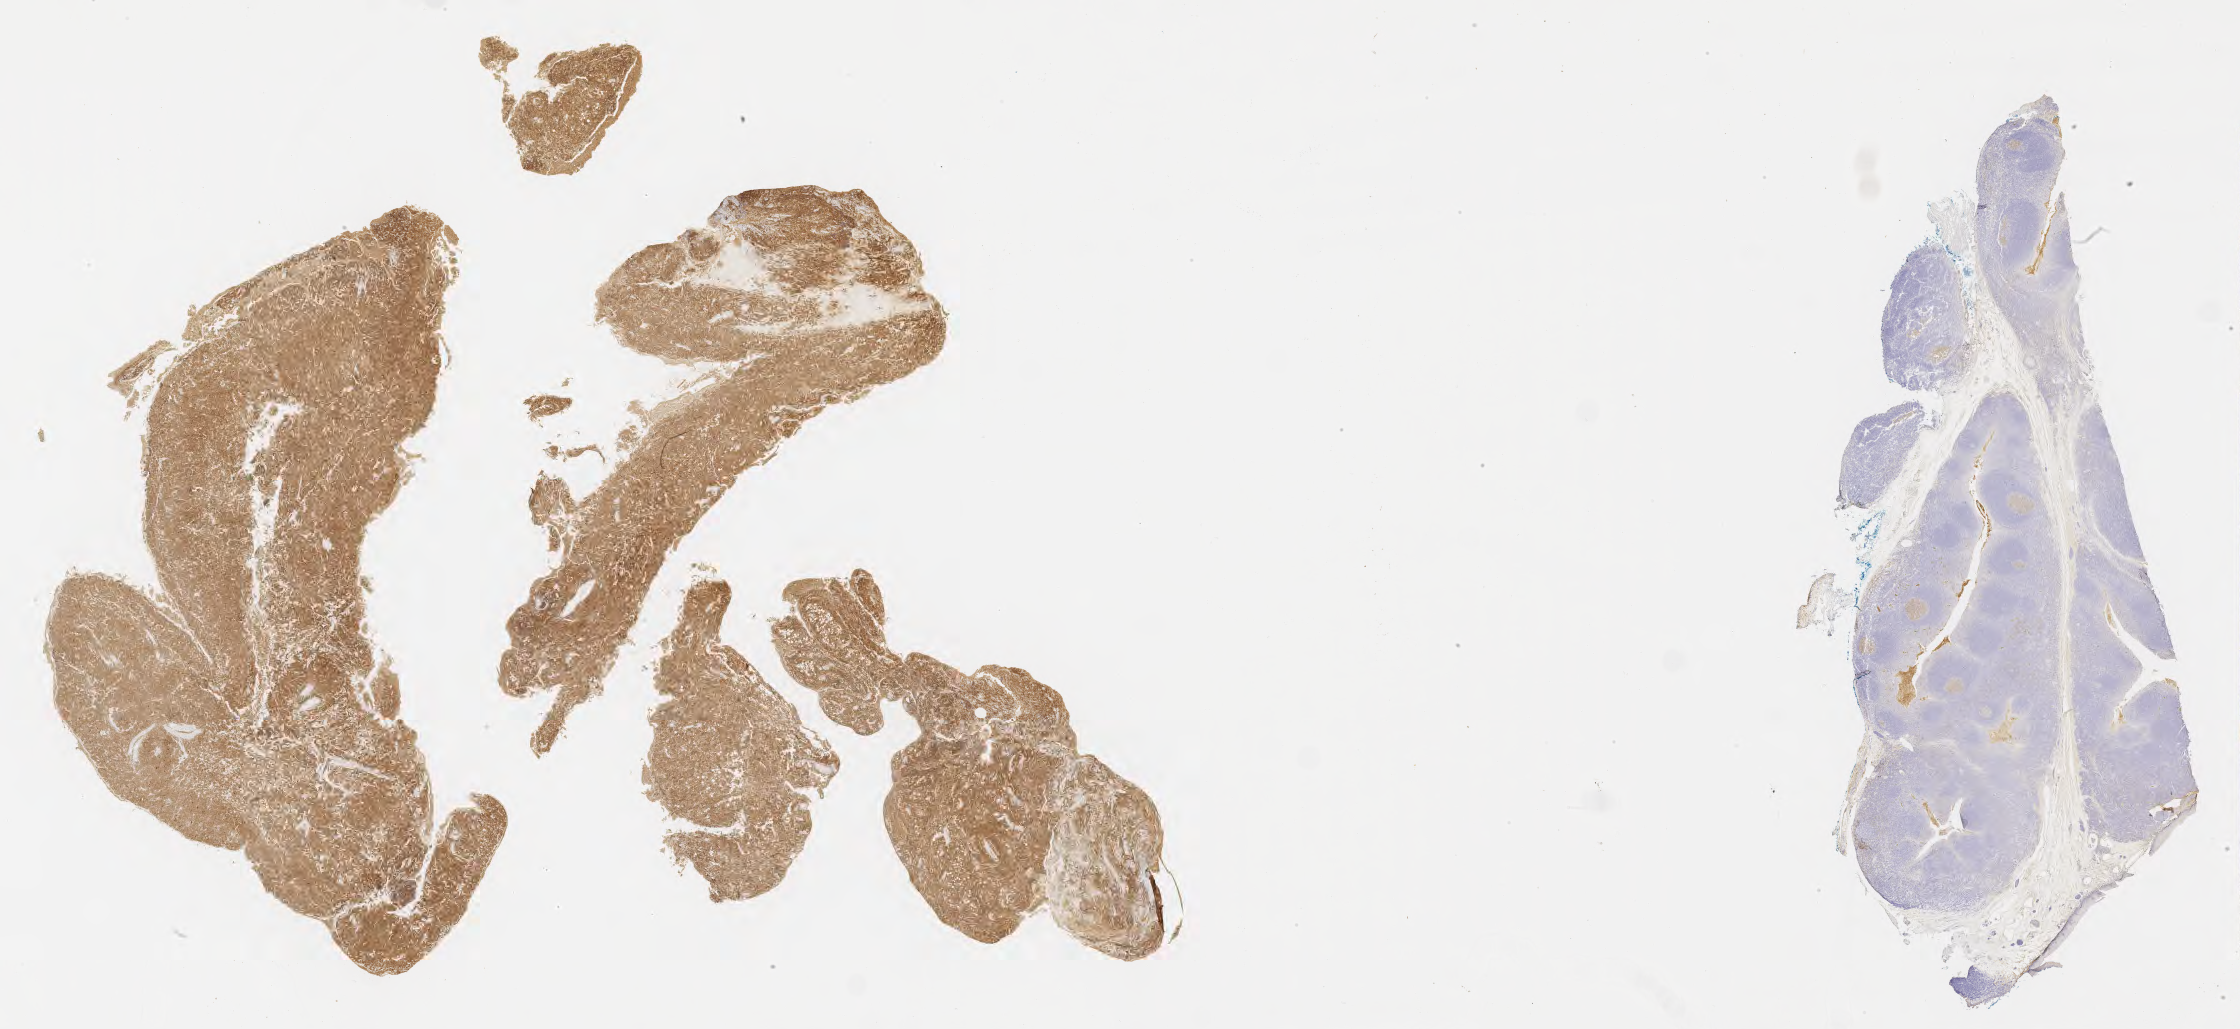
Immunohistochemistry (IHC) whole-slide image stained for CD10, shown as a low-resolution overview of the whole scanned area (about 36.2 x 16.6 mm); tumor tissue; anatomic site: abdomen proper. Patient: male, age at initial diagnosis 5 years.
Diagnosis: Burkitt lymphoma, NOS.